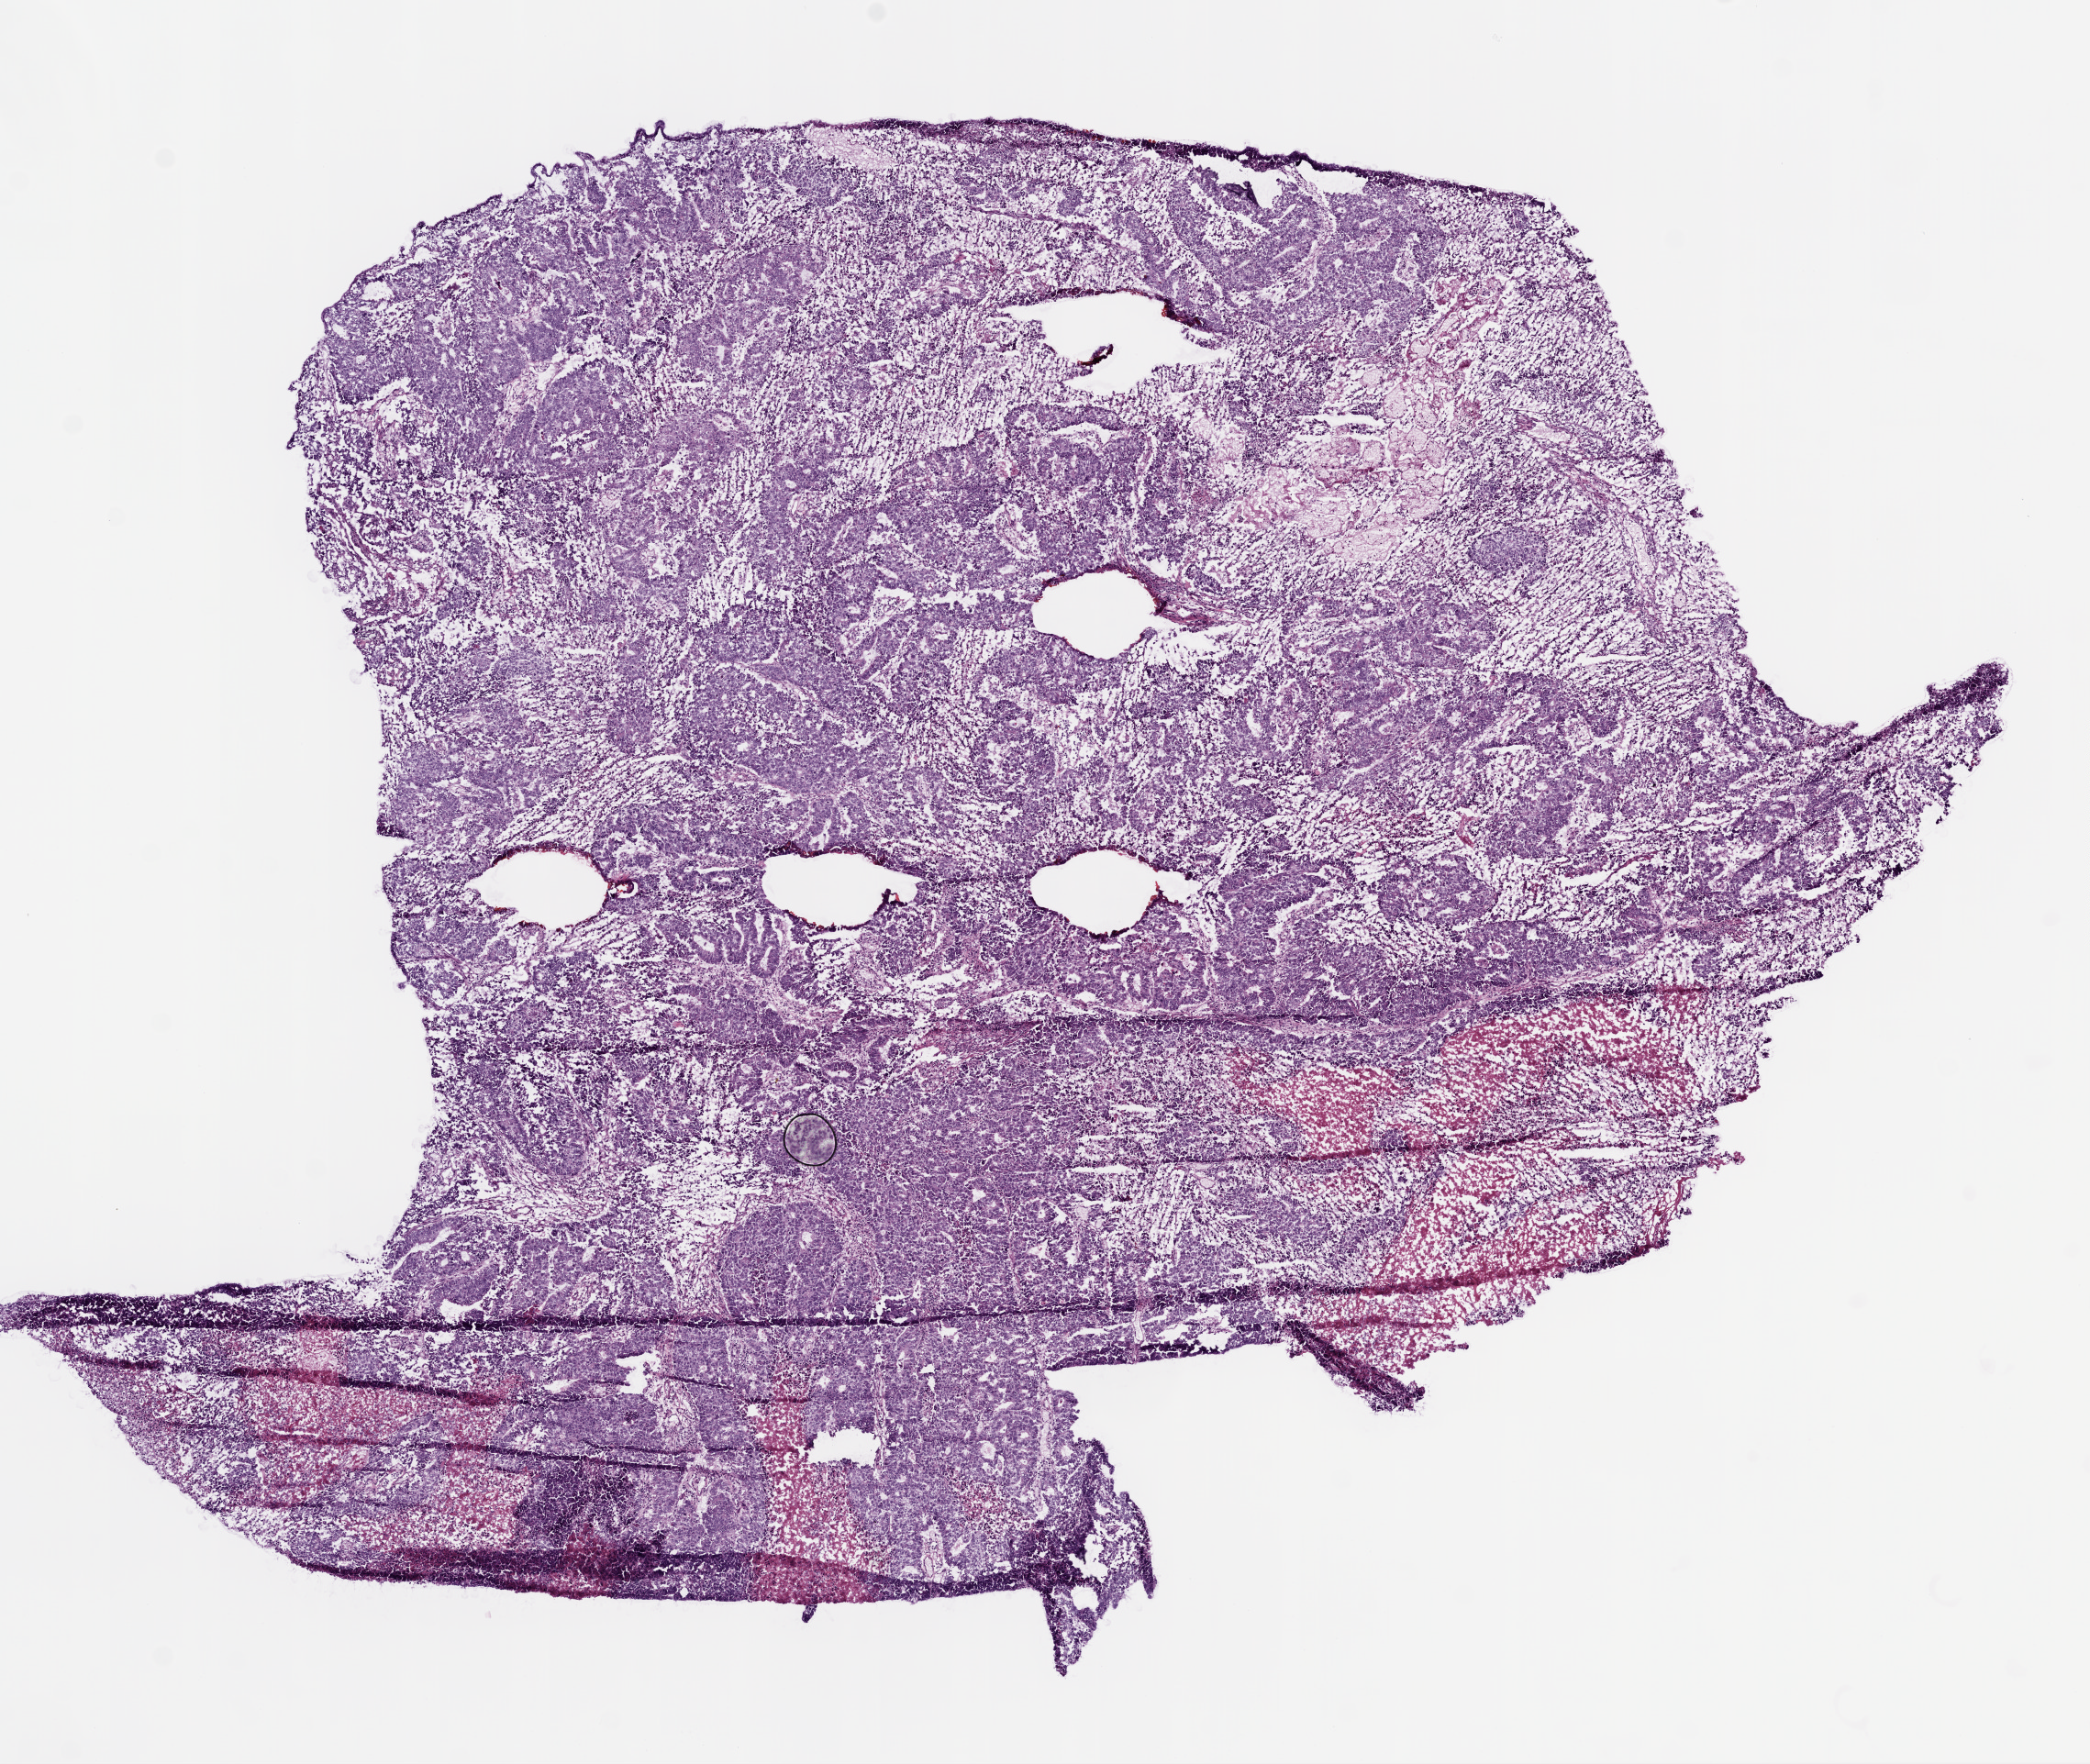
H&E-stained whole-slide image — a low-resolution overview of the entire scanned area, about 9.2 x 7.8 mm. Frozen section from the top of the tissue portion. Uterus, primary tumour sample. Patient: female, age at initial diagnosis 67 years. Pathologist review of this section (percent, as recorded): tumour cells 80%, tumour nuclei 85%.
Pathologic diagnosis: Endometrioid adenocarcinoma, NOS (endometrium).